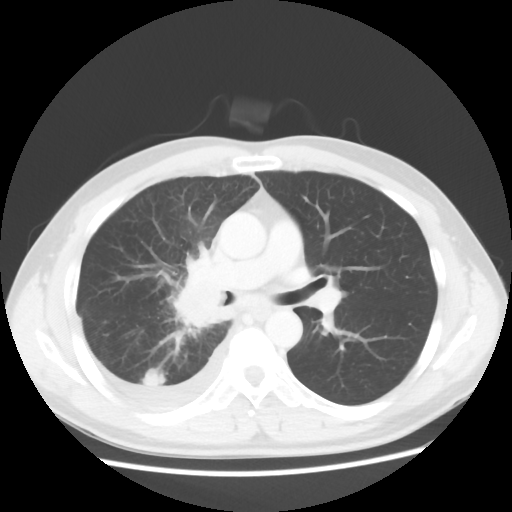
Chest CT, one axial slice; position 32 of 56 along the scan axis; 120 kVp; lung window (W 1500 / L -600 HU); 5 mm slice thickness; 512 × 512 image matrix. Patient: male, 46 years. Case-level facts recorded for this patient, not image findings: clinical TNM (as recorded): T2 N3 M1.
Annotated regions visible in this slice (bounding box drawn by a radiologist):
- lung tumour (recorded histology: adenocarcinoma): bounding box [x1, y1, x2, y2] px = [169, 265, 224, 332]